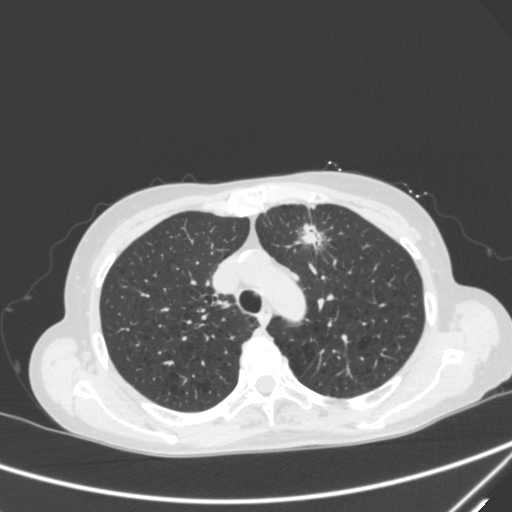
Chest CT, one axial slice; slice 226 of 300 in the series (ordered by position); 120 kVp; lung window (W 1500 / L -600 HU); 512 × 512 image matrix, field of view 350 × 350 mm. Patient: female, 71 years. From the clinical record (not read from this slice): clinical TNM (as recorded): T1c N0 M0; histopathological grade: G2-3.
Outlined on this slice (bounding box drawn by a radiologist):
- lung tumour (recorded histology: adenocarcinoma): bounding box (x1, y1, x2, y2) in pixels: (293, 218, 329, 258)